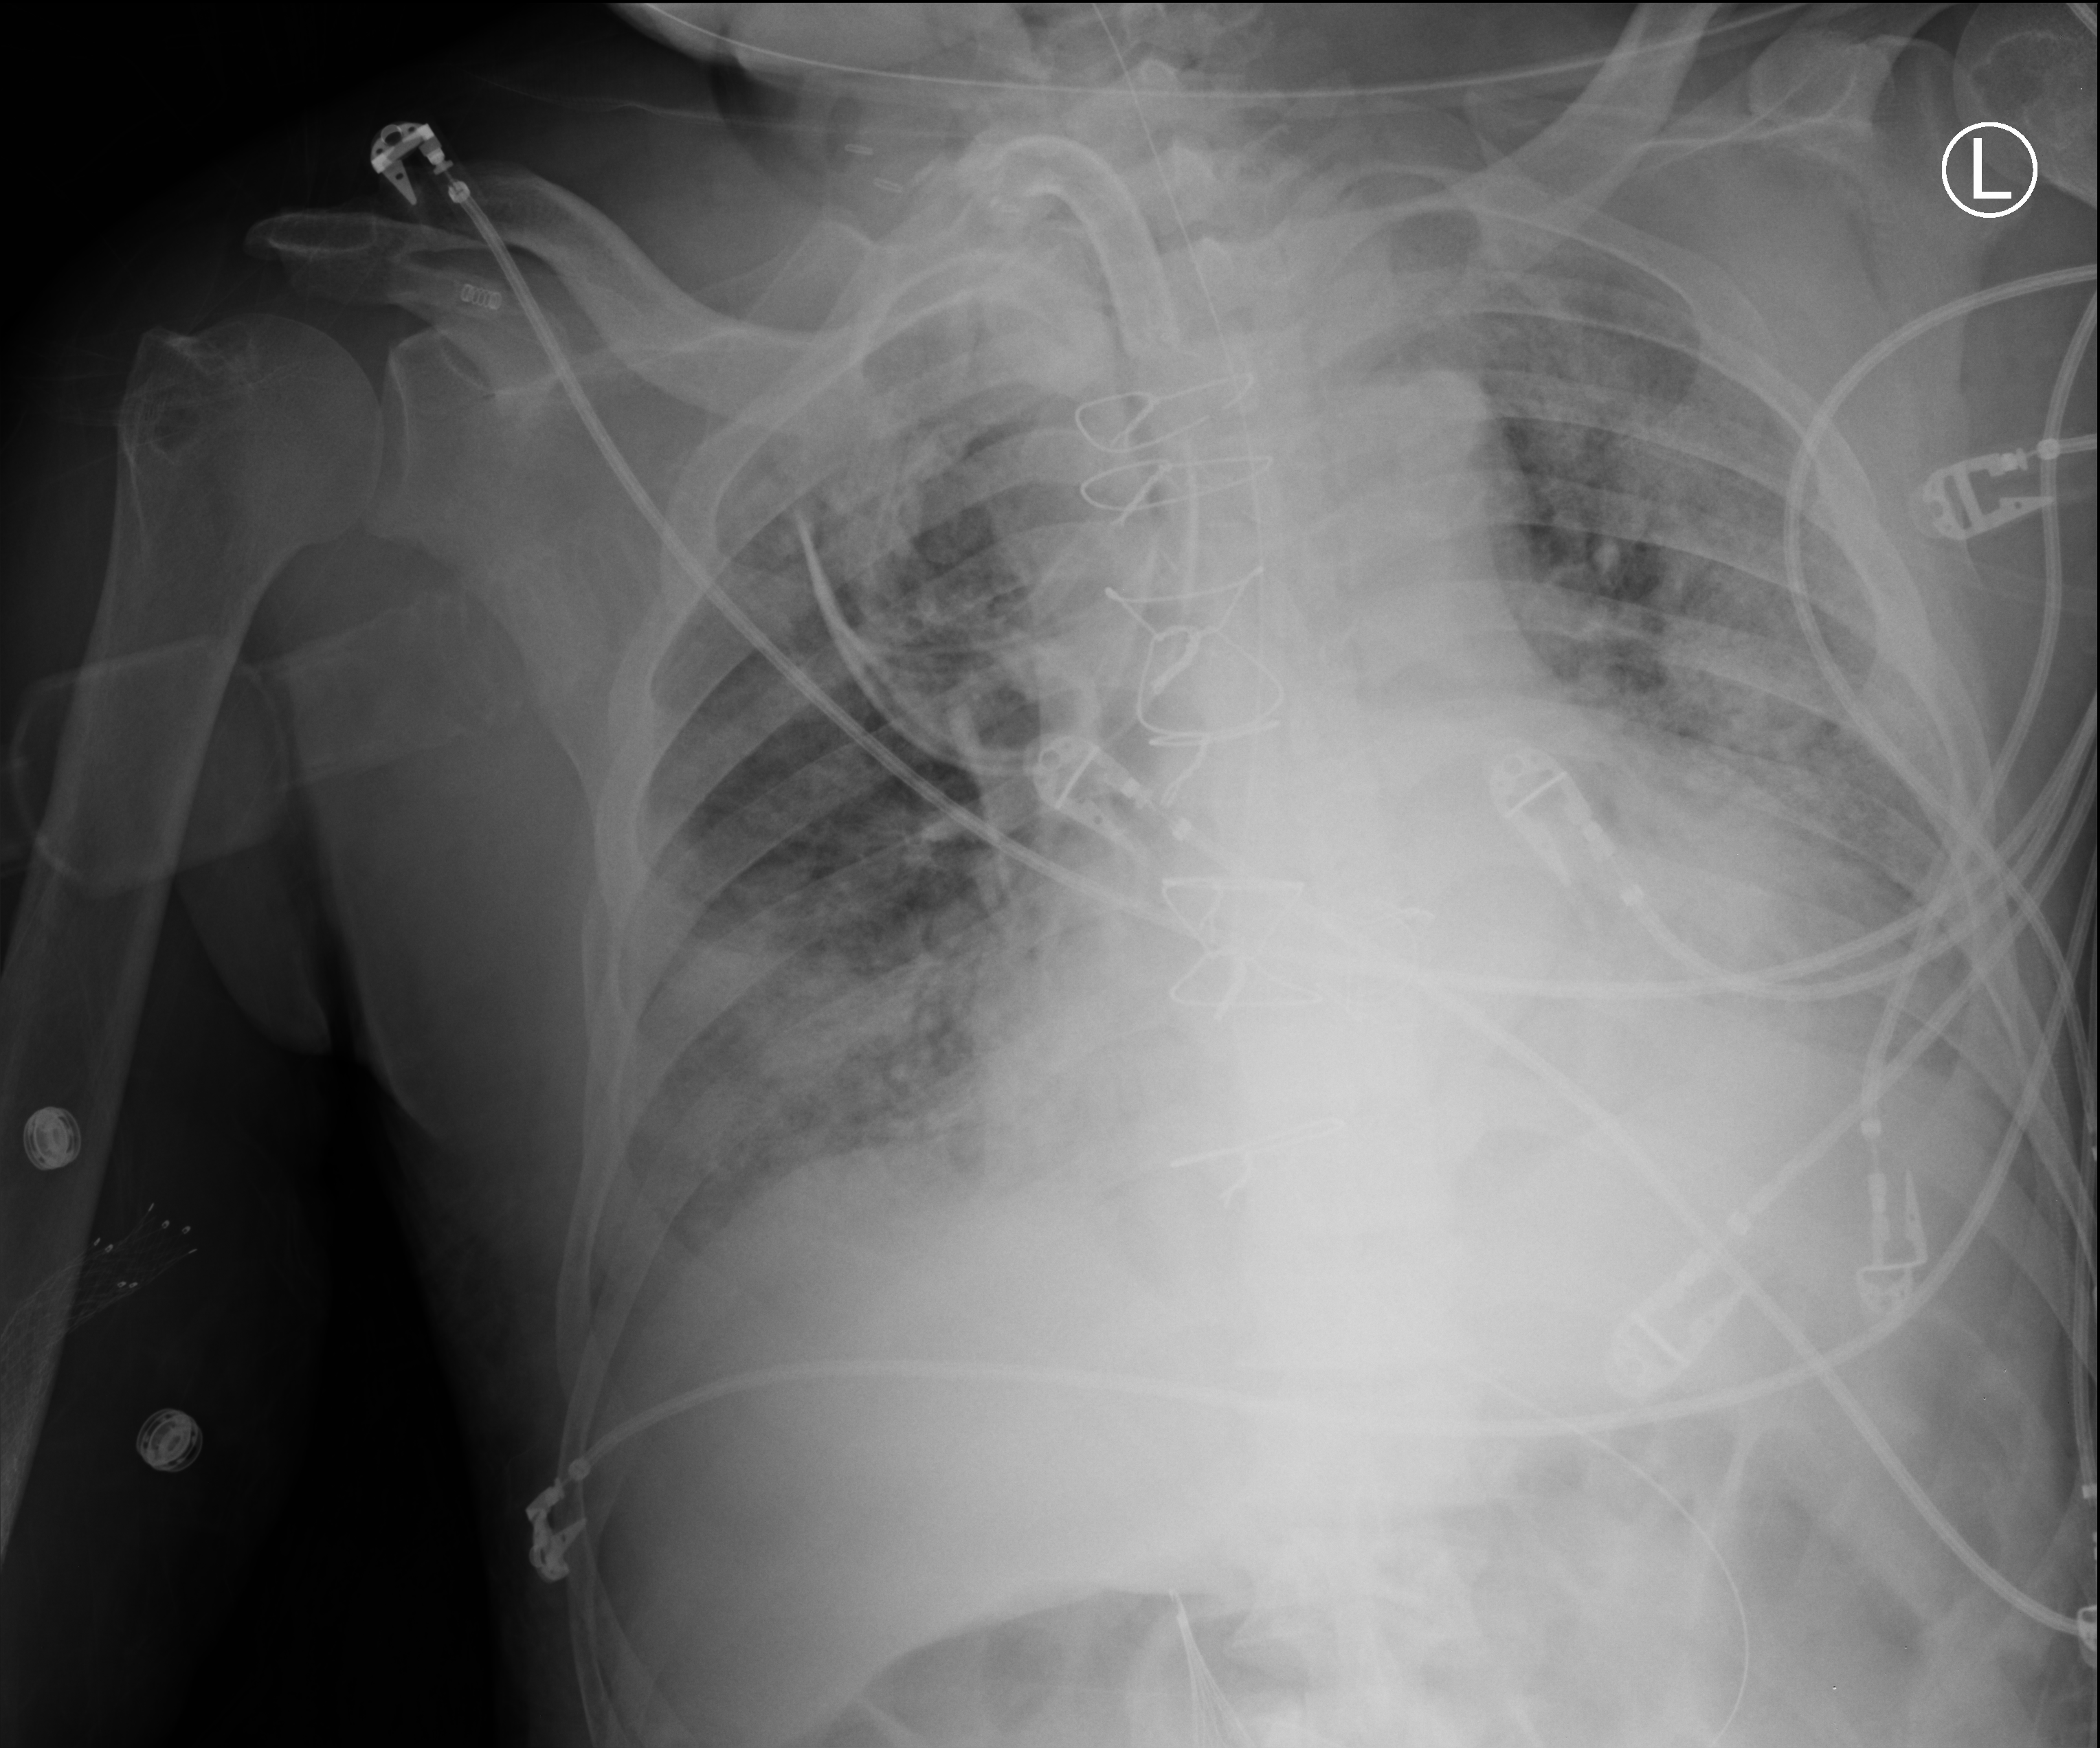
Portable chest radiograph, anteroposterior (AP) projection. Male patient hospitalised with COVID-19, age 60–74 years.
Hospital-stay facts (about this admission, not read from this image; timing relative to this image not recorded):
- mechanically ventilated during this hospital stay: yes